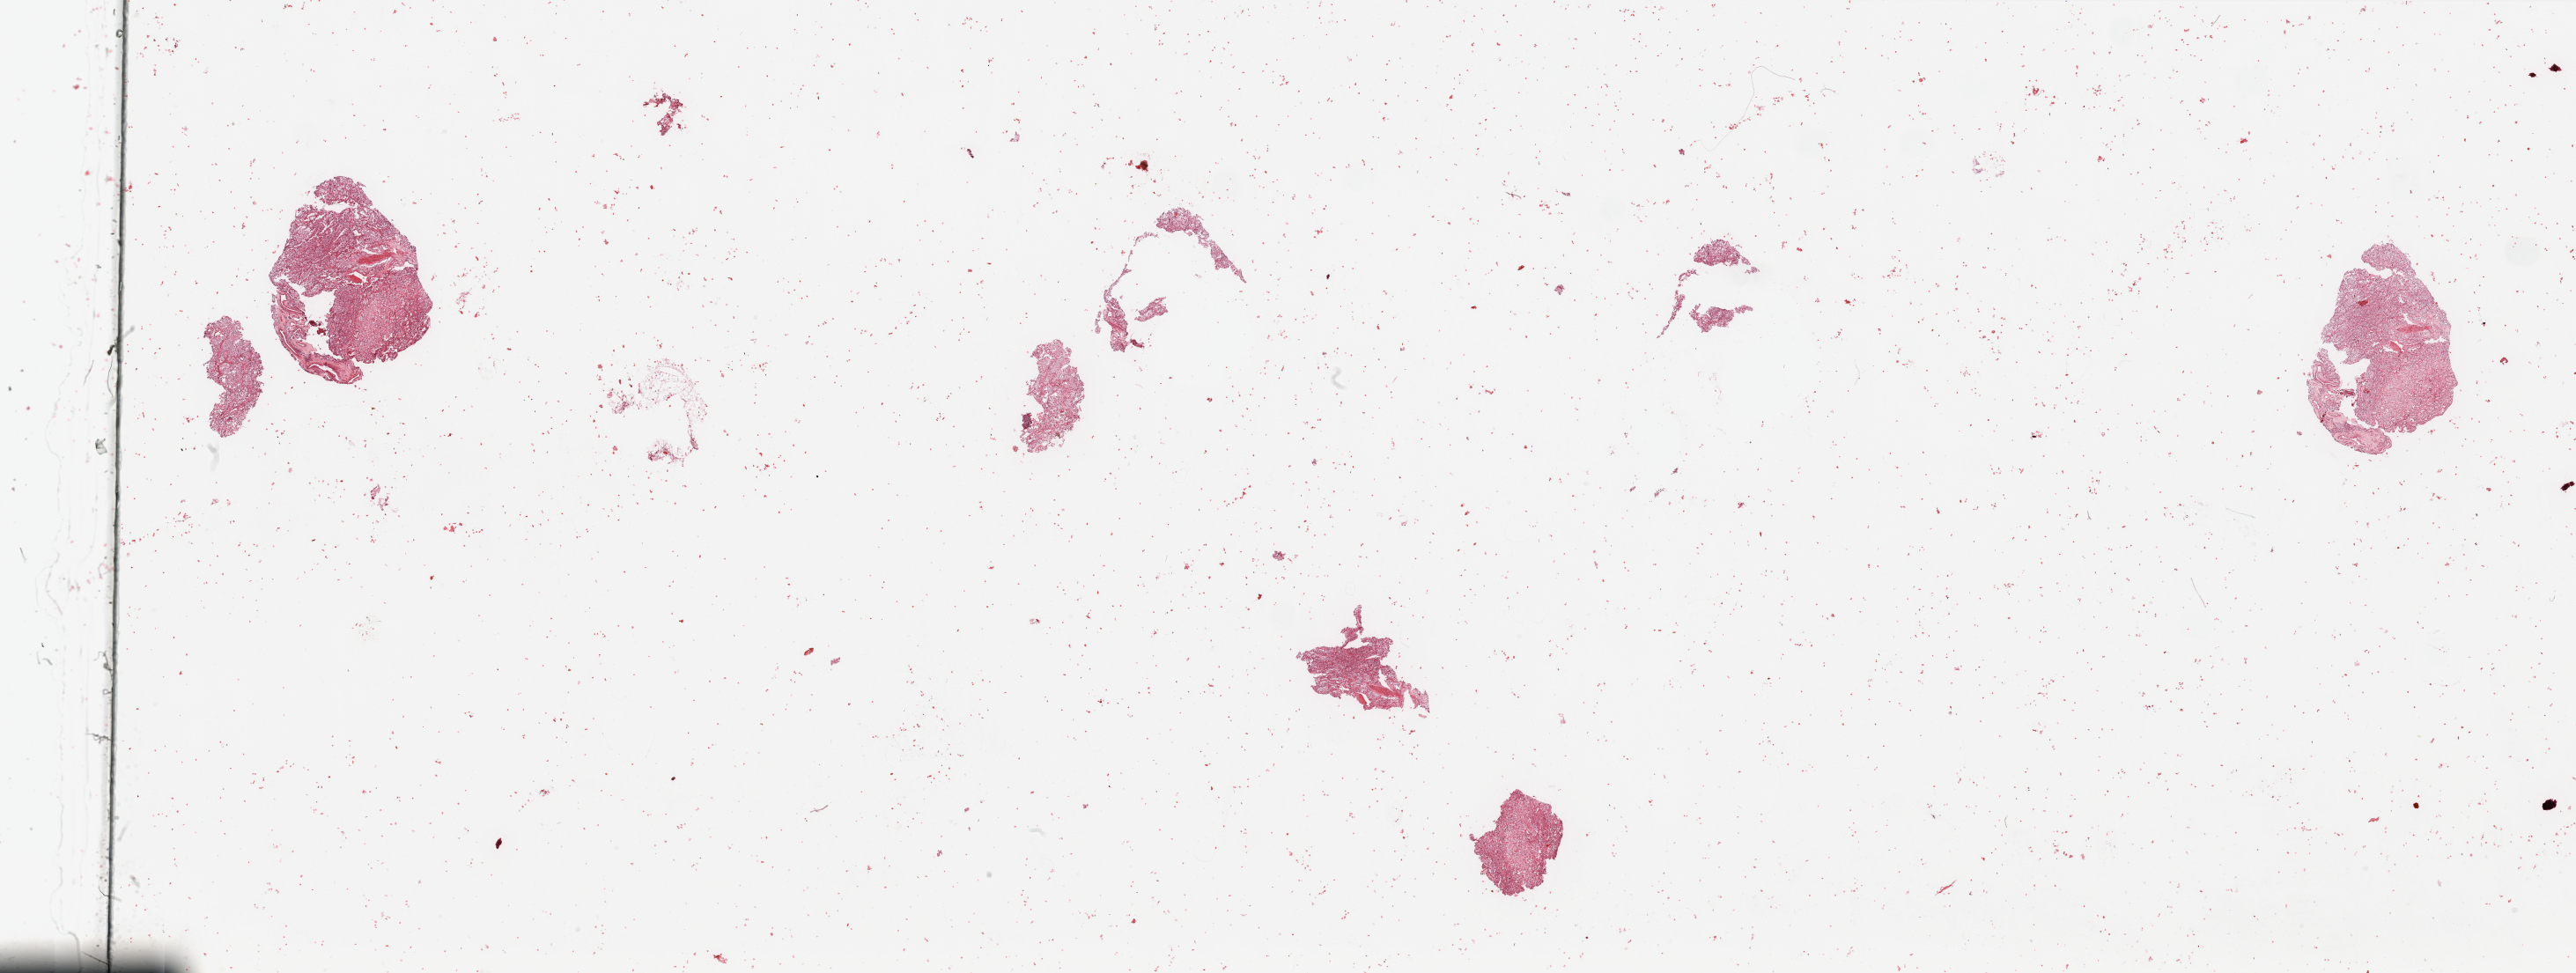
Whole-slide histology image, Hematoxylin and eosin (H&E) stained, a low-resolution overview of the entire scanned area, about 46.3 x 17.5 mm (slide scanned at 20x). Tumour tissue sample, kidney. 68-year-old male patient. Histologic grade: G2 (moderately differentiated).
Histologic diagnosis: Renal cell carcinoma, NOS. Primary tumour site (as recorded): middle. AJCC pathologic stage: III.